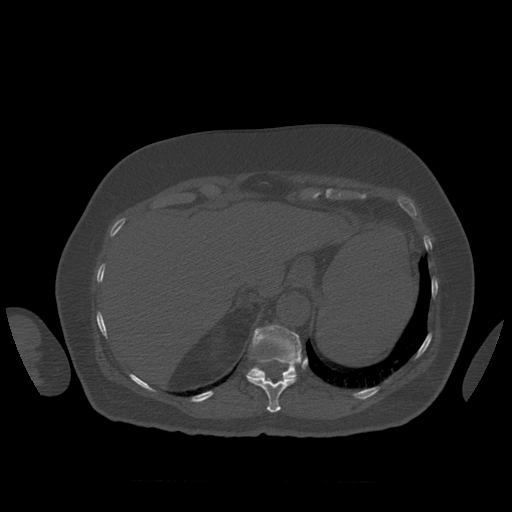
CT including the spine, one axial slice; position 313 of 399 along the scan axis; reconstruction kernel STANDARD; bone window (W 1800 / L 400 HU); 512 × 512 image matrix, field of view 404 × 404 mm. Patient age 81 years. From the clinical record (not read from this slice): primary cancer: renal.
Outlined on this slice (semi-automatic segmentation, software-assisted and operator-edited):
- T11 vertebra: bounding box [x1, y1, x2, y2] px = [247, 361, 296, 413]
- T12 vertebra: [247, 325, 302, 381]